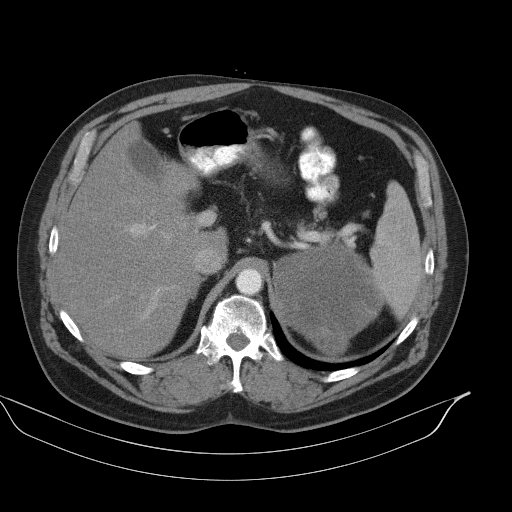
Contrast-enhanced abdominal CT, one axial slice. Position 72 of 92 along the scan axis. 130 kVp. Intravenous contrast given. Soft-tissue window (W 400 / L 40 HU). 512 × 512 image matrix. Male patient, age 56 years. Case-level facts recorded for this patient, not image findings: diagnosis: adrenocortical carcinoma; tumour side: left adrenal; tumour size at pathology: 15 cm; Ki-67 index: 35 %; stage (as recorded): 4.
Outlined on this slice (semi-automatic segmentation, software-assisted and operator-edited):
- mass: bounding box [x1, y1, x2, y2] px = [276, 247, 382, 356]